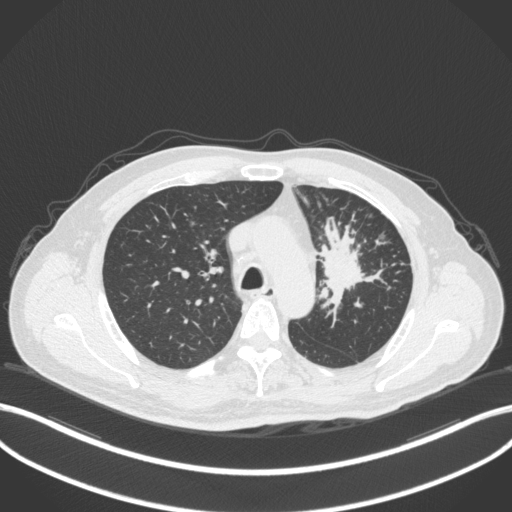
Chest CT, one axial slice. Position 252 of 386 along the scan axis. Reconstruction kernel B31f. 120 kVp. Lung window (W 1500 / L -600 HU). 1 mm slice thickness. 512 × 512 image matrix. Patient: male, 69 years. From the clinical record (not read from this slice): clinical TNM (as recorded): T2a N2 M0; histopathological grade: G2-3.
Structures marked on this image (rectangle marked by the reading radiologist):
- lung tumour (recorded histology: adenocarcinoma): bounding box <313,216,380,319> (left, top, right, bottom; pixels)